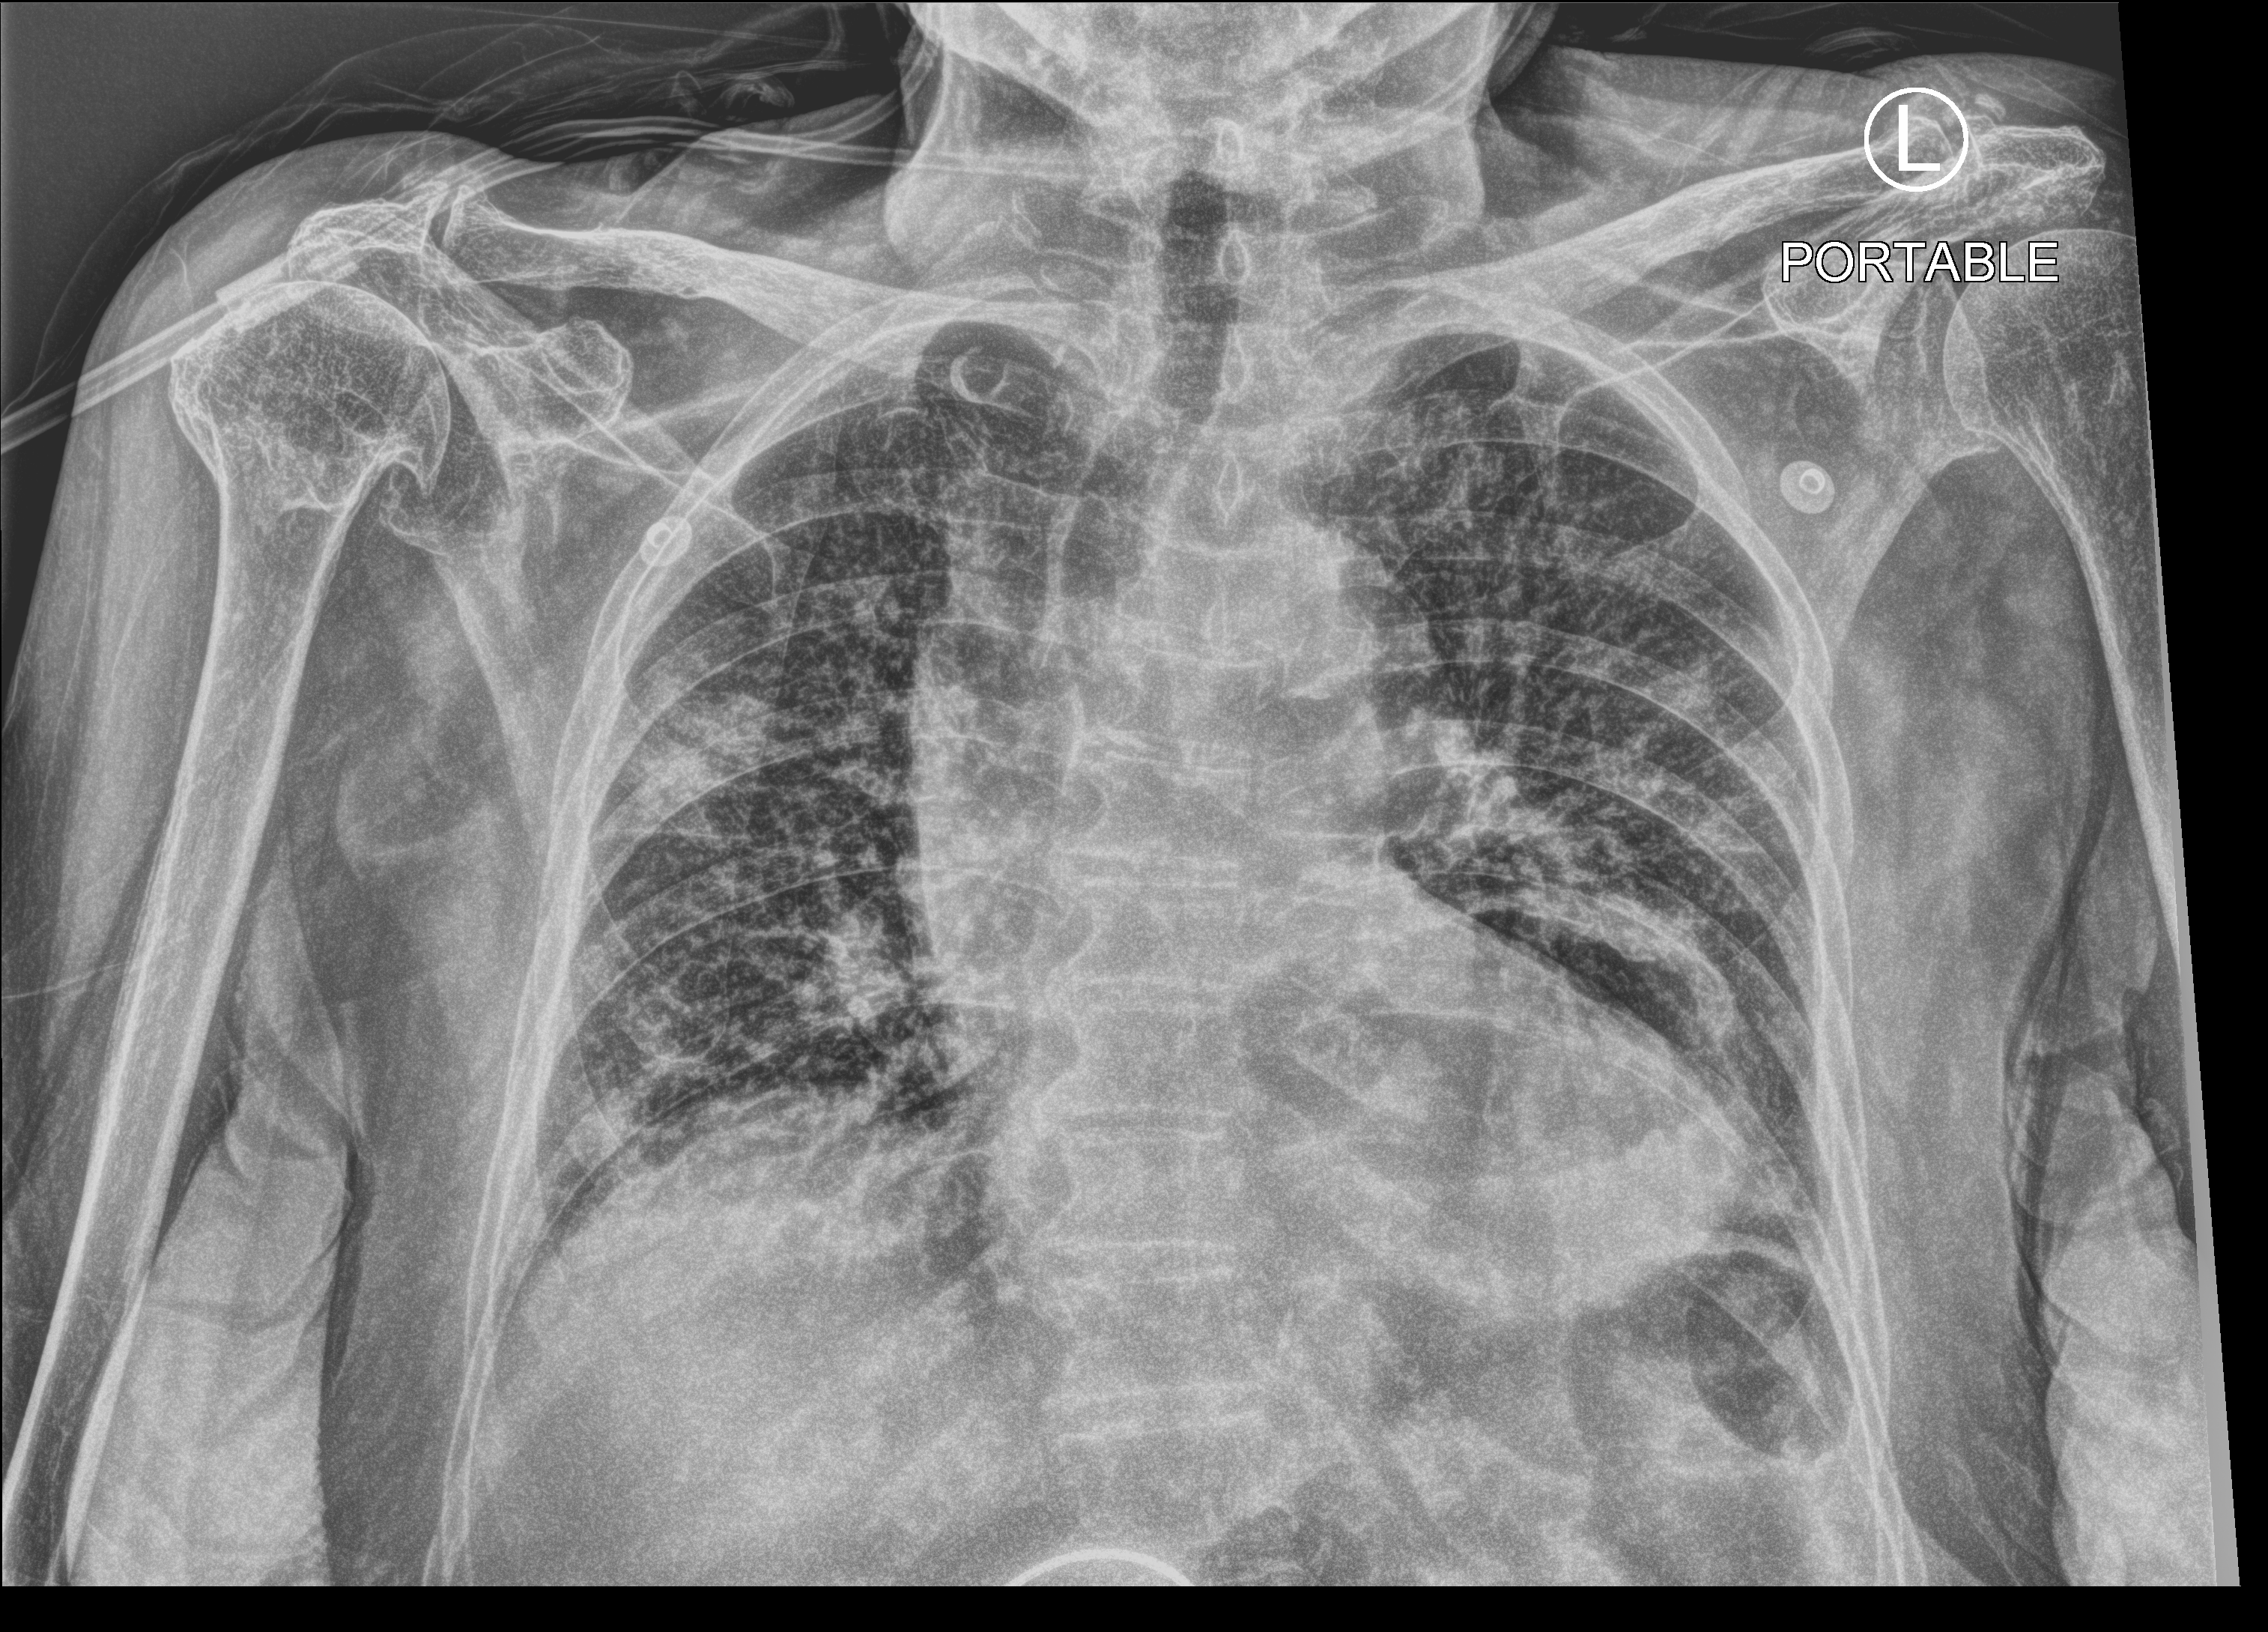
Portable chest radiograph, anteroposterior (AP) projection. Patient hospitalised with COVID-19; female, aged 75–90 years.
Admission-level facts for this patient (not findings on this image; timing relative to this image not recorded):
- length of hospital stay: 9 days